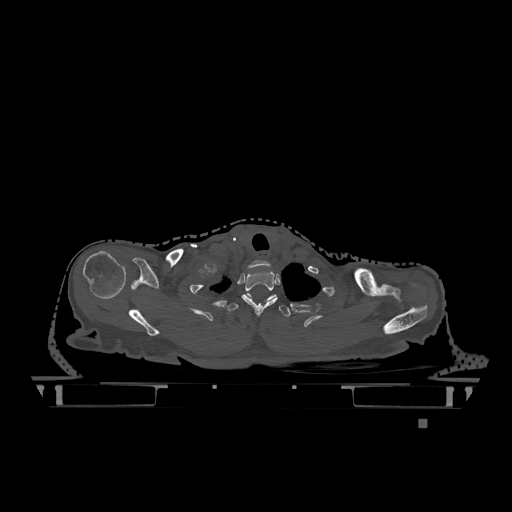
CT including the spine, one axial slice; position 990 of 1317 along the scan axis; bone window (W 1800 / L 400 HU); 0.5 mm slice thickness; 512 × 512 image matrix, field of view 500 × 500 mm. Female patient, age 74 years. From the clinical record (not read from this slice): primary cancer: lung.
Structures marked on this image (semi-automatically segmented with operator editing):
- T1 vertebra: box from (x=241, y=271) to (x=278, y=316) px
- T2 vertebra: (x=227, y=295)–(x=291, y=317)